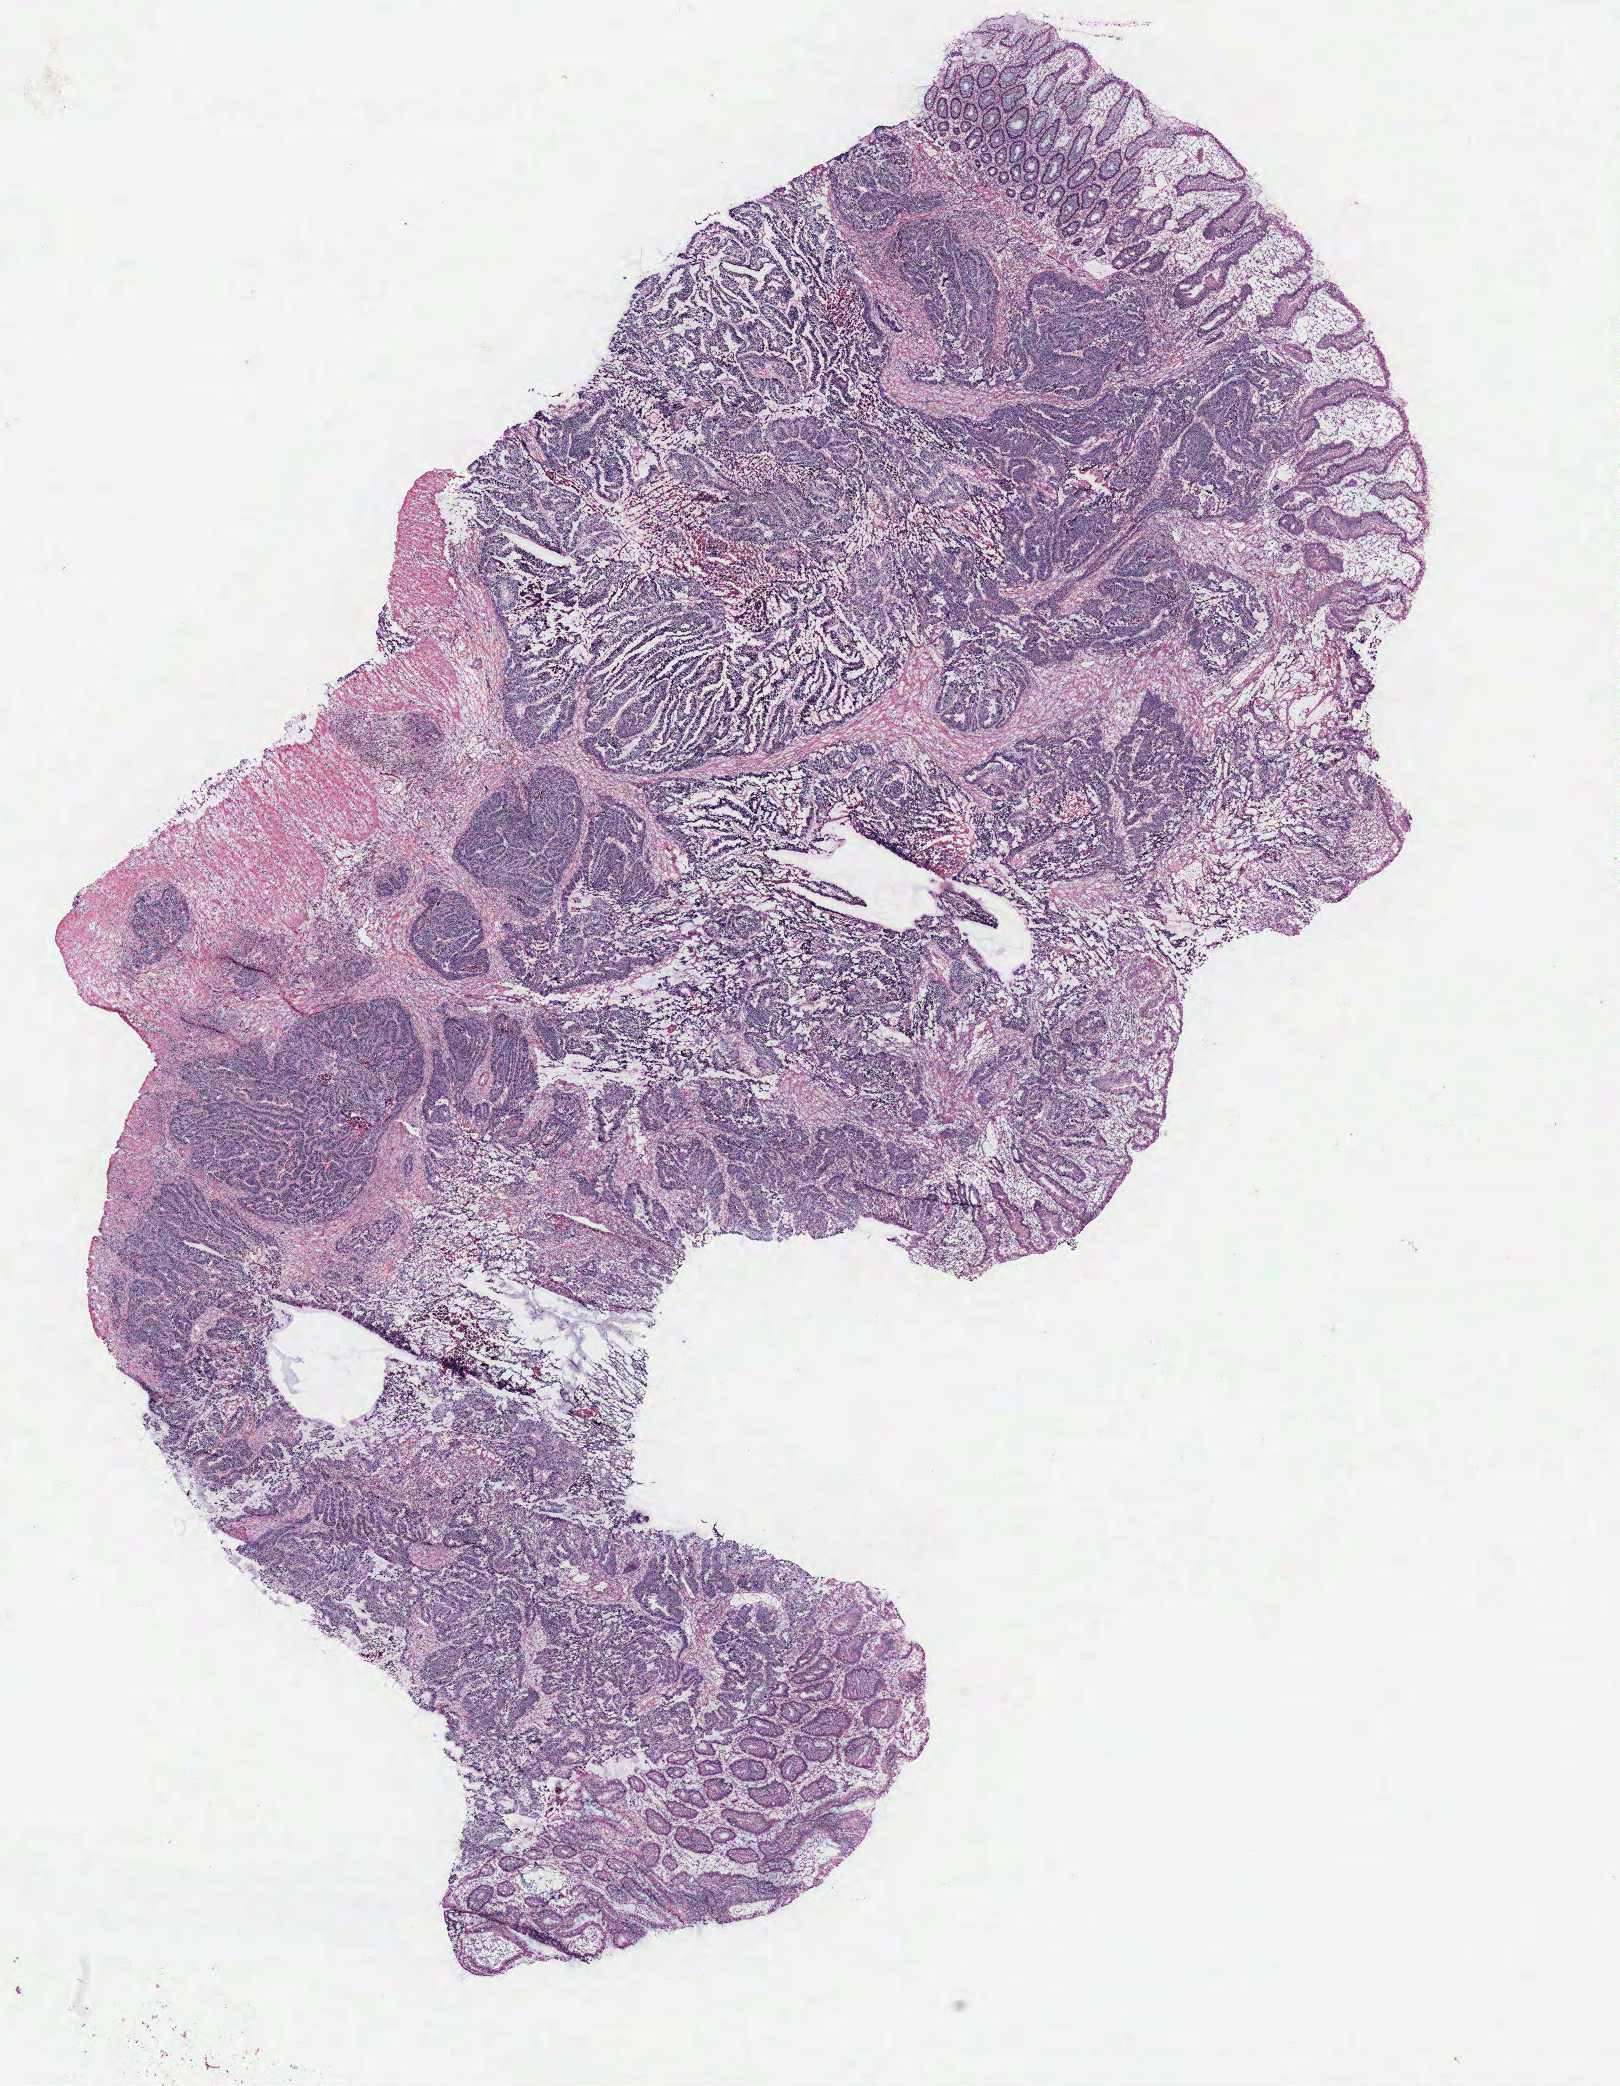
Whole-slide histology image, H&E — low-resolution overview of the scanned area, about 13.0 x 16.7 mm (slide scanned at 40x); colon, normal (non-tumour) tissue. 39-year-old male patient.
This section: normal (non-tumour) tissue from the same patient. Patient diagnosis: Adenocarcinoma, NOS.